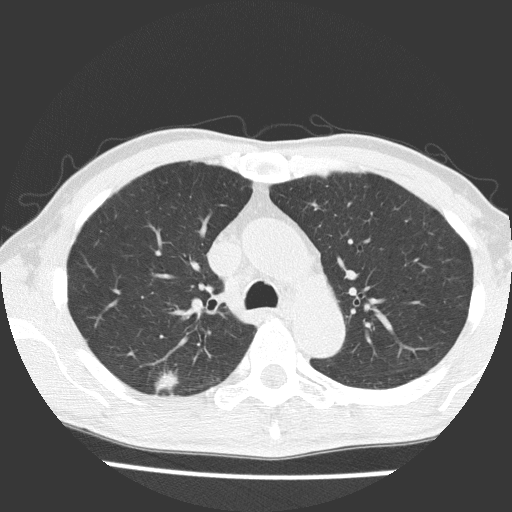
Chest CT (low-dose screening protocol), one axial image; first (baseline) screen; lung window (W 1500 / L -600 HU); 120 kVp. Male, age 66 years at enrolment. Current smoker at enrolment.
- Expert reader's lesion annotation, box from (x=137, y=357) to (x=194, y=409) px.
- Reader record for this screening exam (exam-level; its link to the box is not recorded): non-calcified nodule or mass ≥4 mm, right upper lobe, 15 × 10 mm, spiculated (stellate) margins, soft tissue attenuation.
- Lung cancer was diagnosed 43 days after this screen: adenocarcinoma, NOS, right upper lobe, moderately differentiated (G2), stage IB (AJCC 6th edition), 11 mm at pathology.